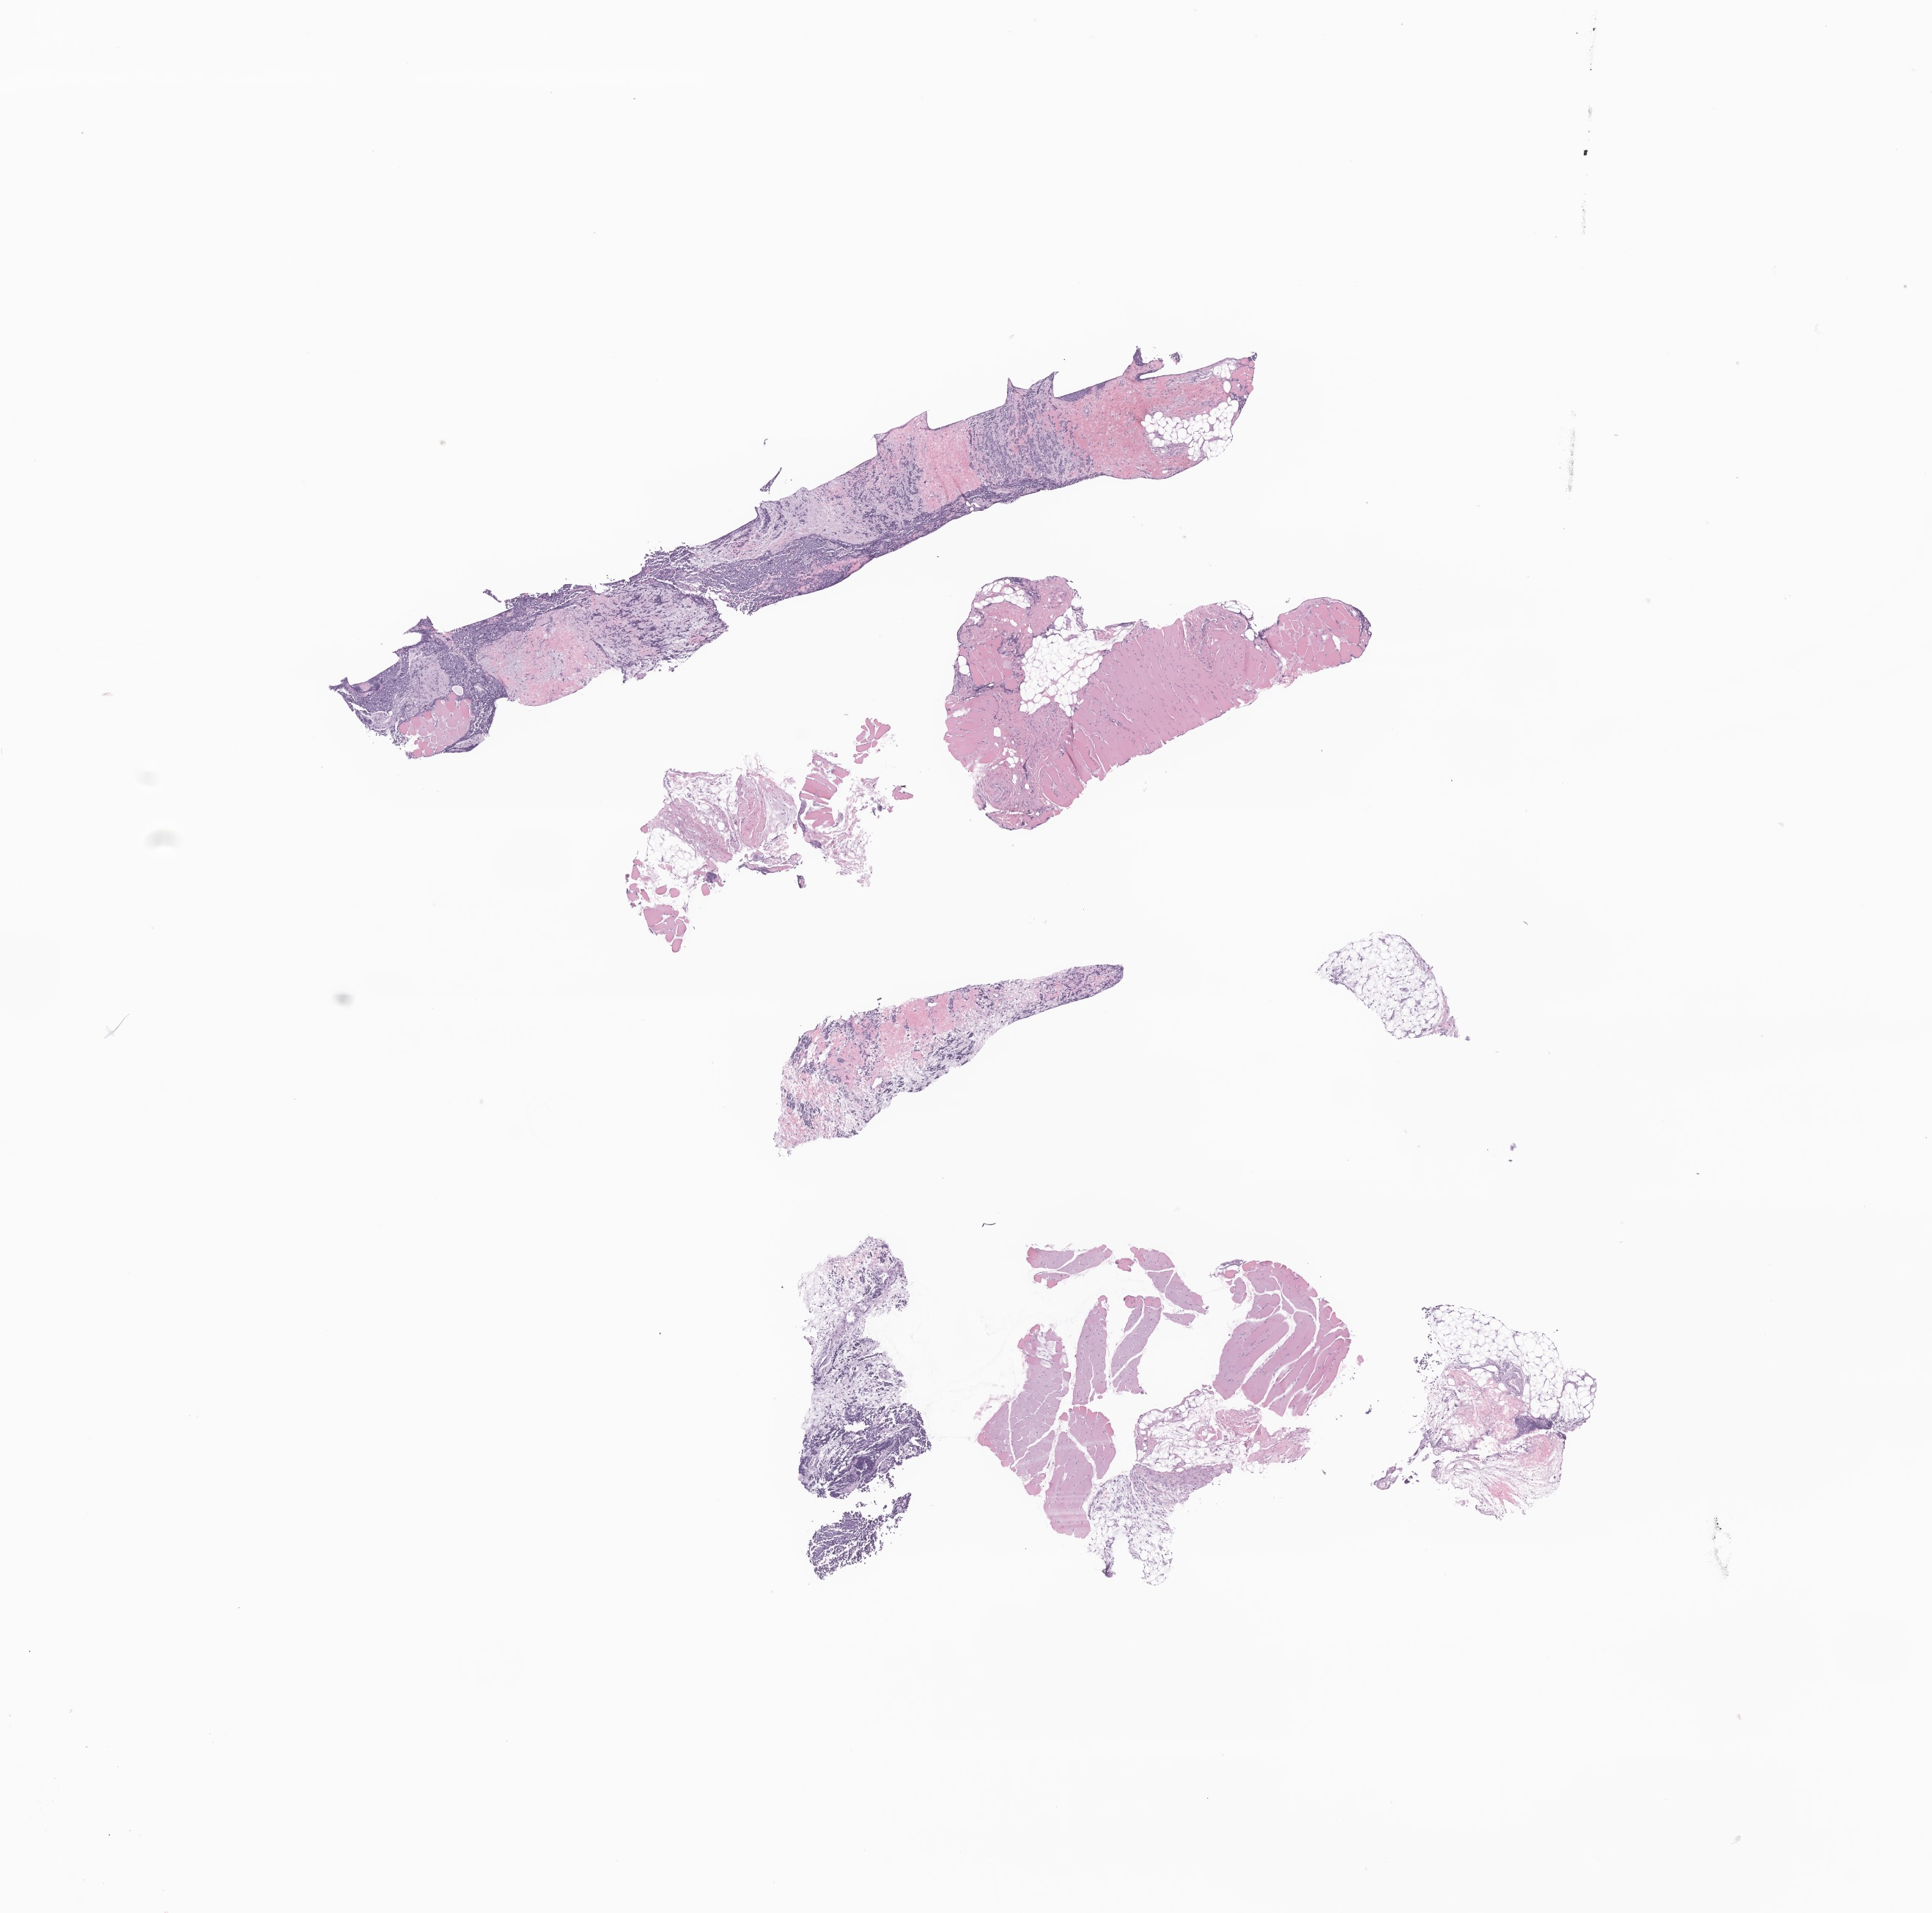
Digitized hematoxylin and eosin (H&E)-stained section of tumor tissue from the adrenal gland, shown as a low-resolution overview of the whole scanned area (about 11.1 x 11.0 mm); formalin-fixed, paraffin-embedded (FFPE) tissue. Patient male; age 117 months (9 years 9 months).
Diagnosis (ICD-O-3 morphology term): Neuroblastoma, NOS.